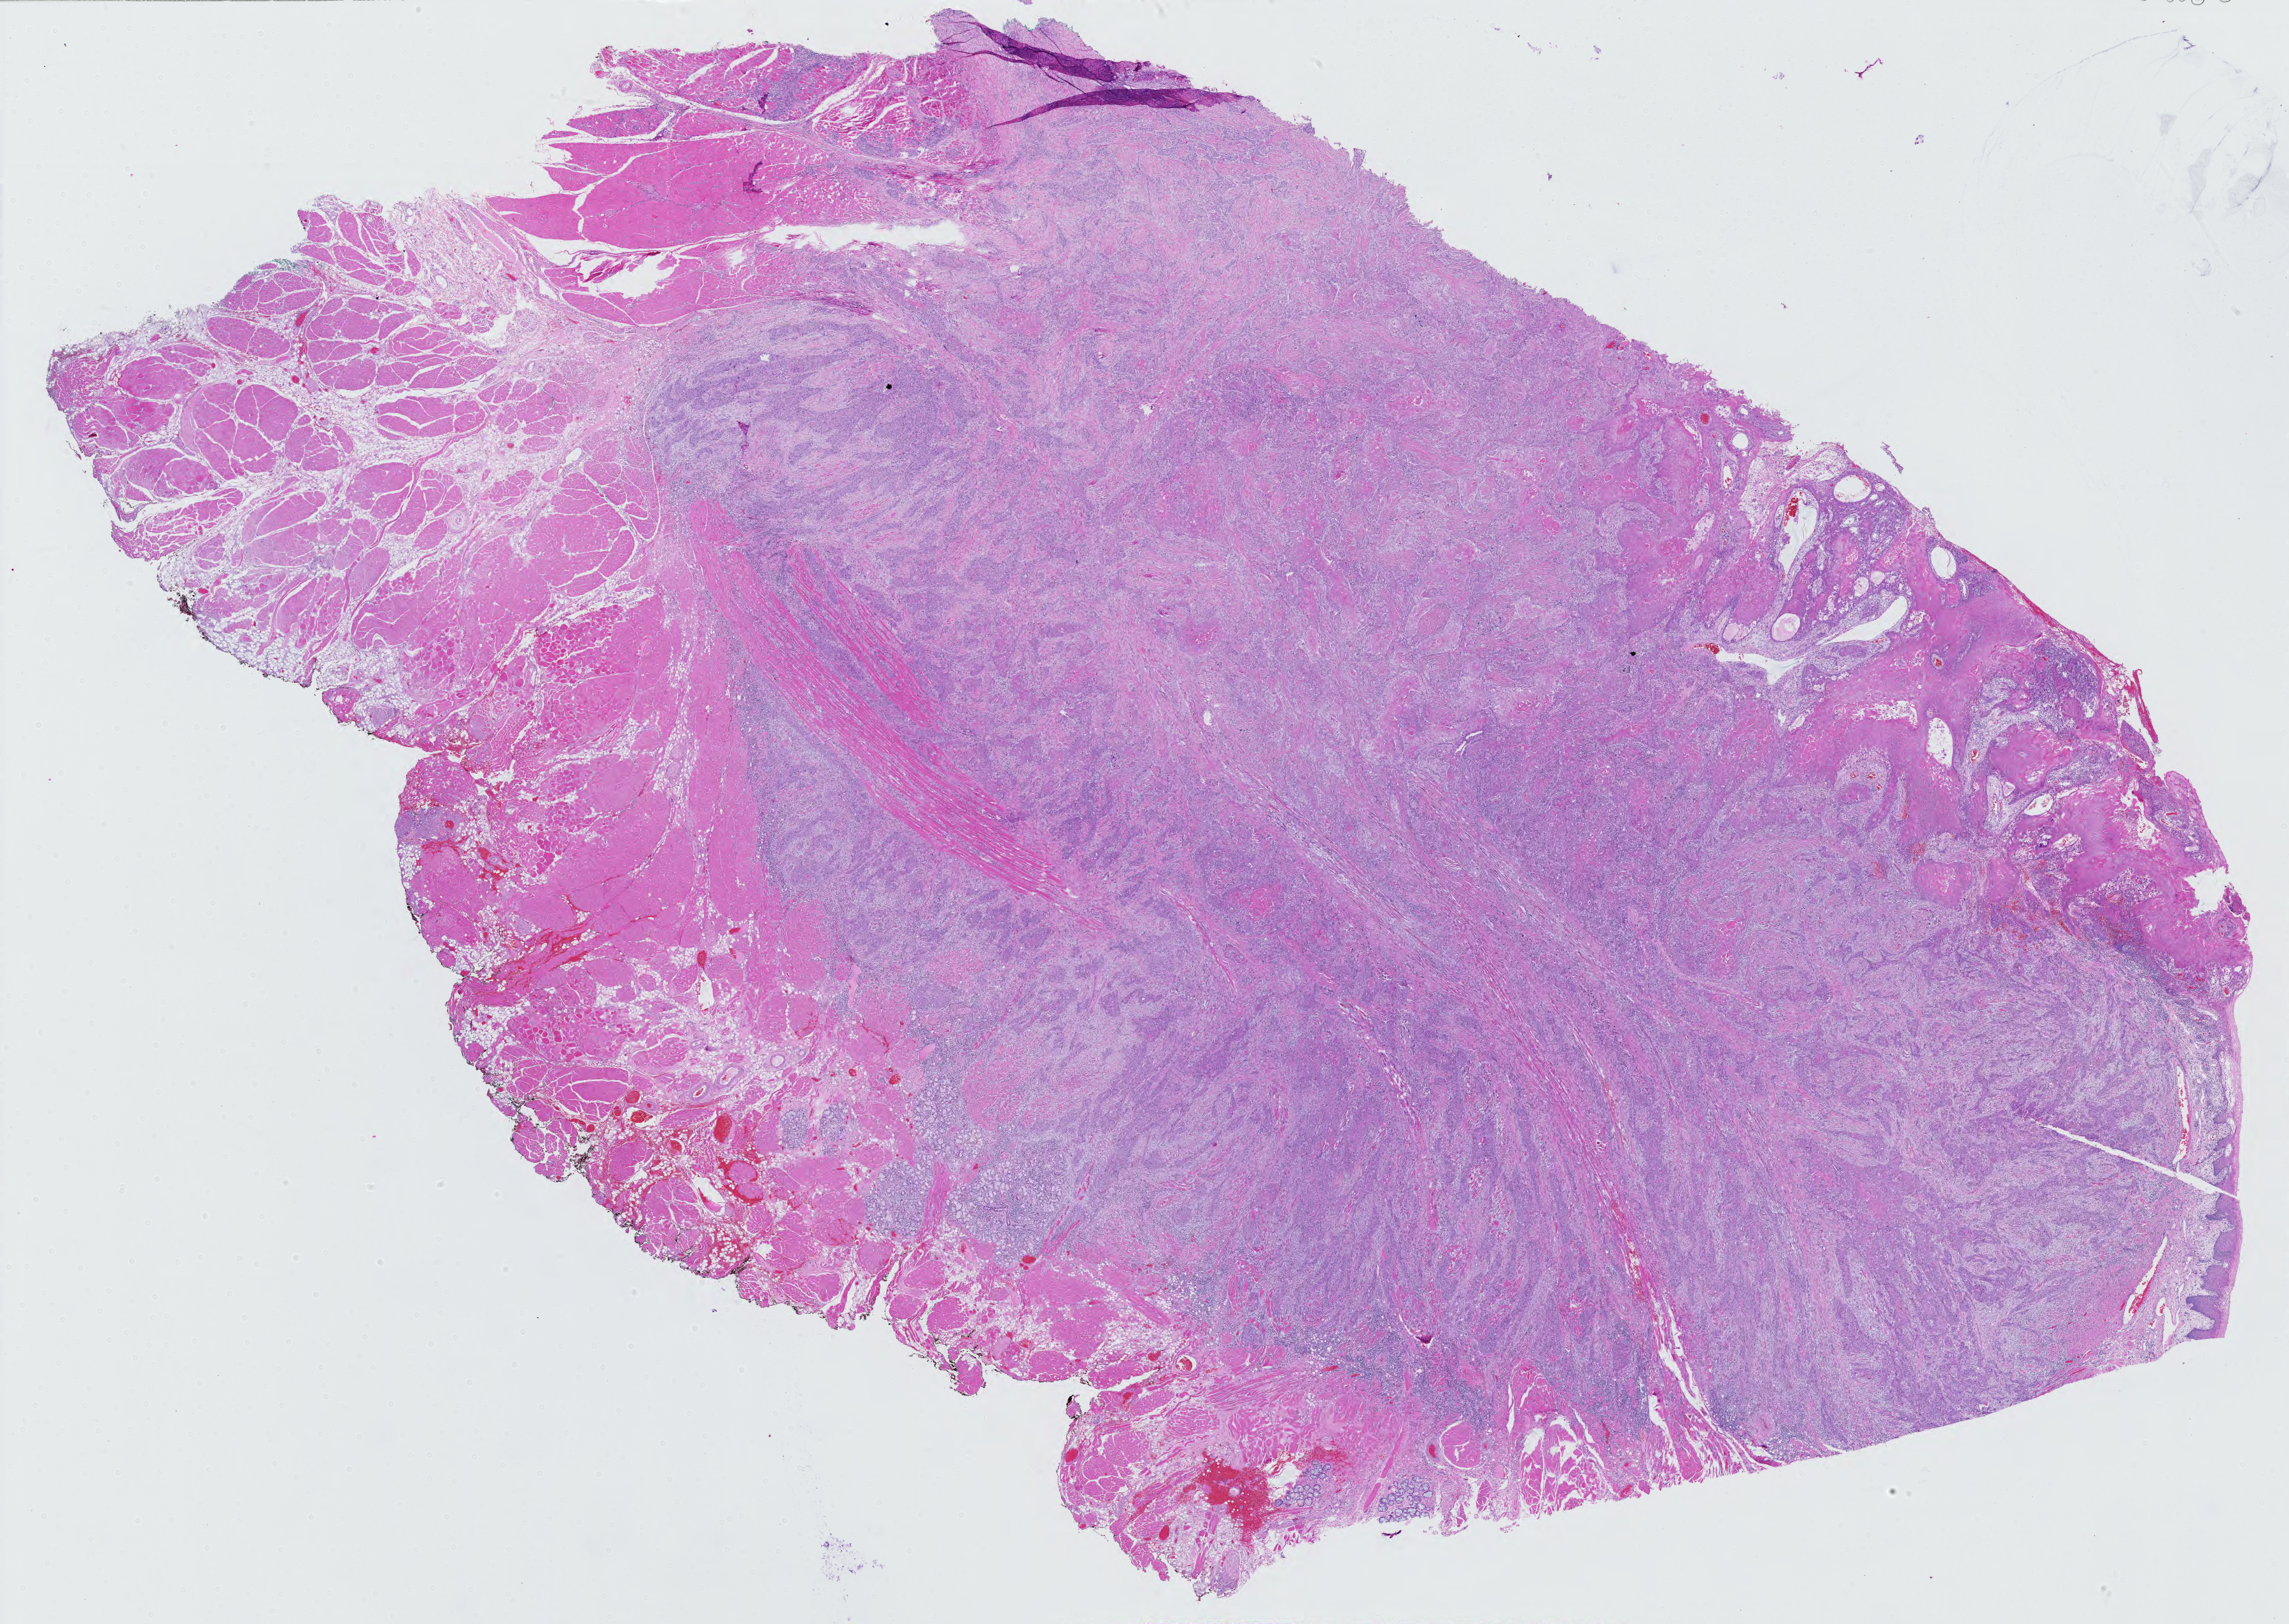
H&E-stained whole-slide image — whole scanned area (about 26.1 x 18.5 mm, acquisition: 40x scan) shown as a low-resolution overview, FFPE section, primary tumour sample from the head and neck. Male, age 60 years at initial diagnosis. Histologic grade: G2 (moderately differentiated).
Diagnosis: Squamous cell carcinoma, NOS (tongue, NOS). Laterality: right. AJCC pathologic stage: IVA (7th edition).